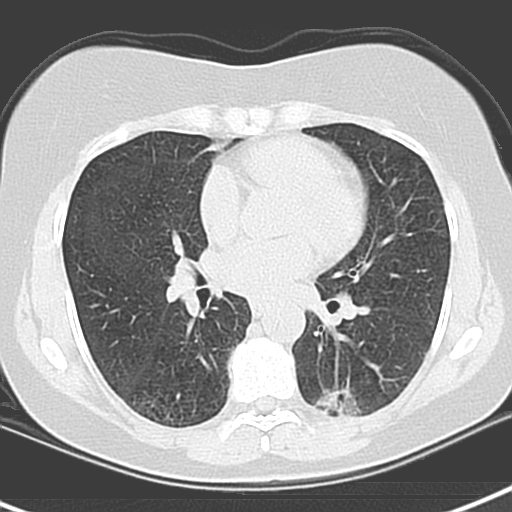
Chest CT (low-dose screening protocol), one axial image. Baseline screening round. Lung window (W 1500 / L -600 HU). 512 × 512 image matrix. Female participant, aged 55 years at enrolment. Current smoker at enrolment.
Lesion marked by an expert reader, bounding box <311,374,387,424> (left, top, right, bottom; pixels). The screening reader recorded 3 non-calcified nodules or masses ≥4 mm on this exam (left upper lobe, left lower lobe, left lower lobe); which of them this box marks is not recorded. Participant outcome: lung cancer diagnosed 1063 days after this screen — adenocarcinoma with mixed subtypes, left lower lobe, poorly differentiated (G3), stage IA (AJCC 6th edition), 21 mm at pathology.